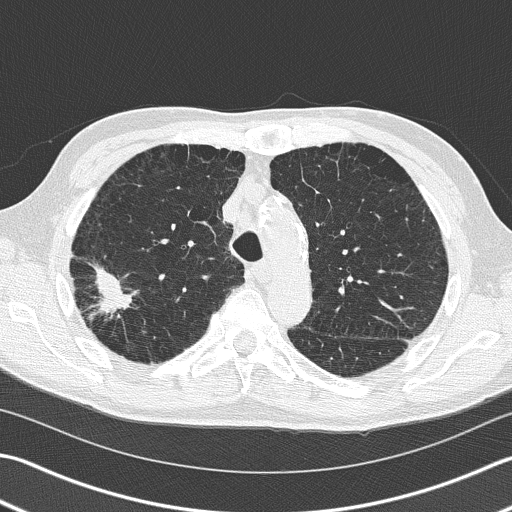
Chest CT (low-dose screening protocol), one axial image, first (baseline) screen, lung window (W 1500 / L -600 HU). Male, age 66 years at enrolment.
Lesion marked by an expert reader, bounding box [x1, y1, x2, y2] px = [66, 247, 138, 339]. Reader record for this screening exam (exam-level; its link to the box is not recorded): non-calcified nodule or mass ≥4 mm, right upper lobe, 39 × 23 mm, spiculated (stellate) margins, soft tissue attenuation. Official screen result: positive, change unspecified: nodule(s) >= 4 mm or enlarging nodule(s), mass(es), or other non-specific abnormalities suspicious for lung cancer. Lung cancer was diagnosed 36 days after this screen: squamous cell carcinoma, NOS, right upper lobe, poorly differentiated (G3), stage IB (AJCC 6th edition), 23 mm at pathology.